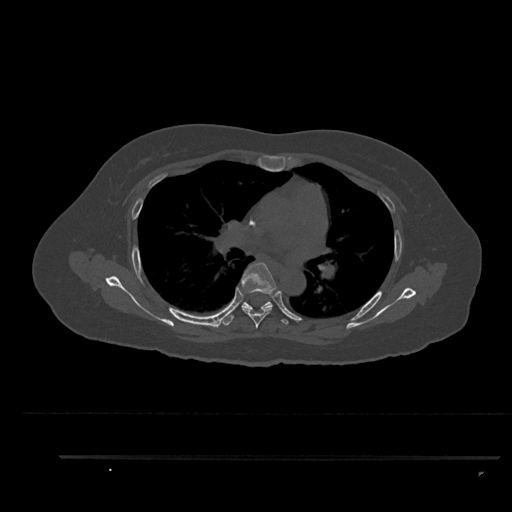
CT including the spine, one axial slice; slice 583 of 797 in the series (ordered by position); reconstruction kernel Br40s/3; 120 kVp; bone window (W 1800 / L 400 HU); 0.5 mm slice thickness; 512 × 512 image matrix, field of view 408 × 408 mm. Patient: female, 44 years. From the clinical record (not read from this slice): primary cancer: renal; vertebrae with lytic lesions (as recorded): L1.
Outlined on this slice (semi-automatically segmented with operator editing):
- T5 vertebra: box from (x=241, y=262) to (x=276, y=329) px
- T6 vertebra: (x=223, y=301)–(x=289, y=326)